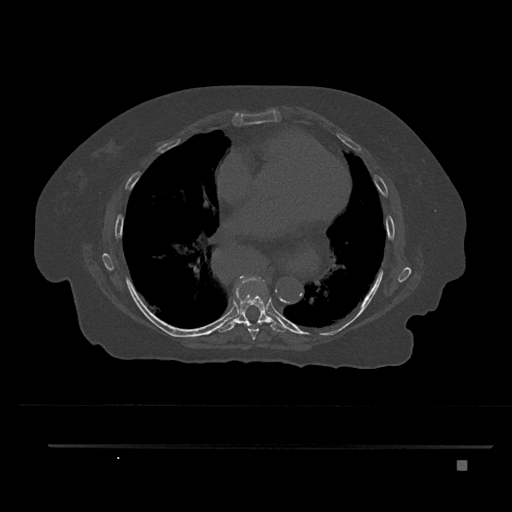
CT including the spine, one axial slice. Slice 460 of 797 in the series (ordered by position). Reconstruction kernel Br40s/3. Bone window (W 1800 / L 400 HU). 512 × 512 image matrix, field of view 437 × 437 mm. Patient: female, 76 years. From the clinical record (not read from this slice): primary cancer: lung; vertebrae with lytic lesions (as recorded): T11, L3.
Outlined on this slice (semi-automatic segmentation, software-assisted and operator-edited):
- T7 vertebra: bounding box (x1, y1, x2, y2) in pixels: (238, 277, 263, 340)
- T8 vertebra: (218, 277, 289, 333)